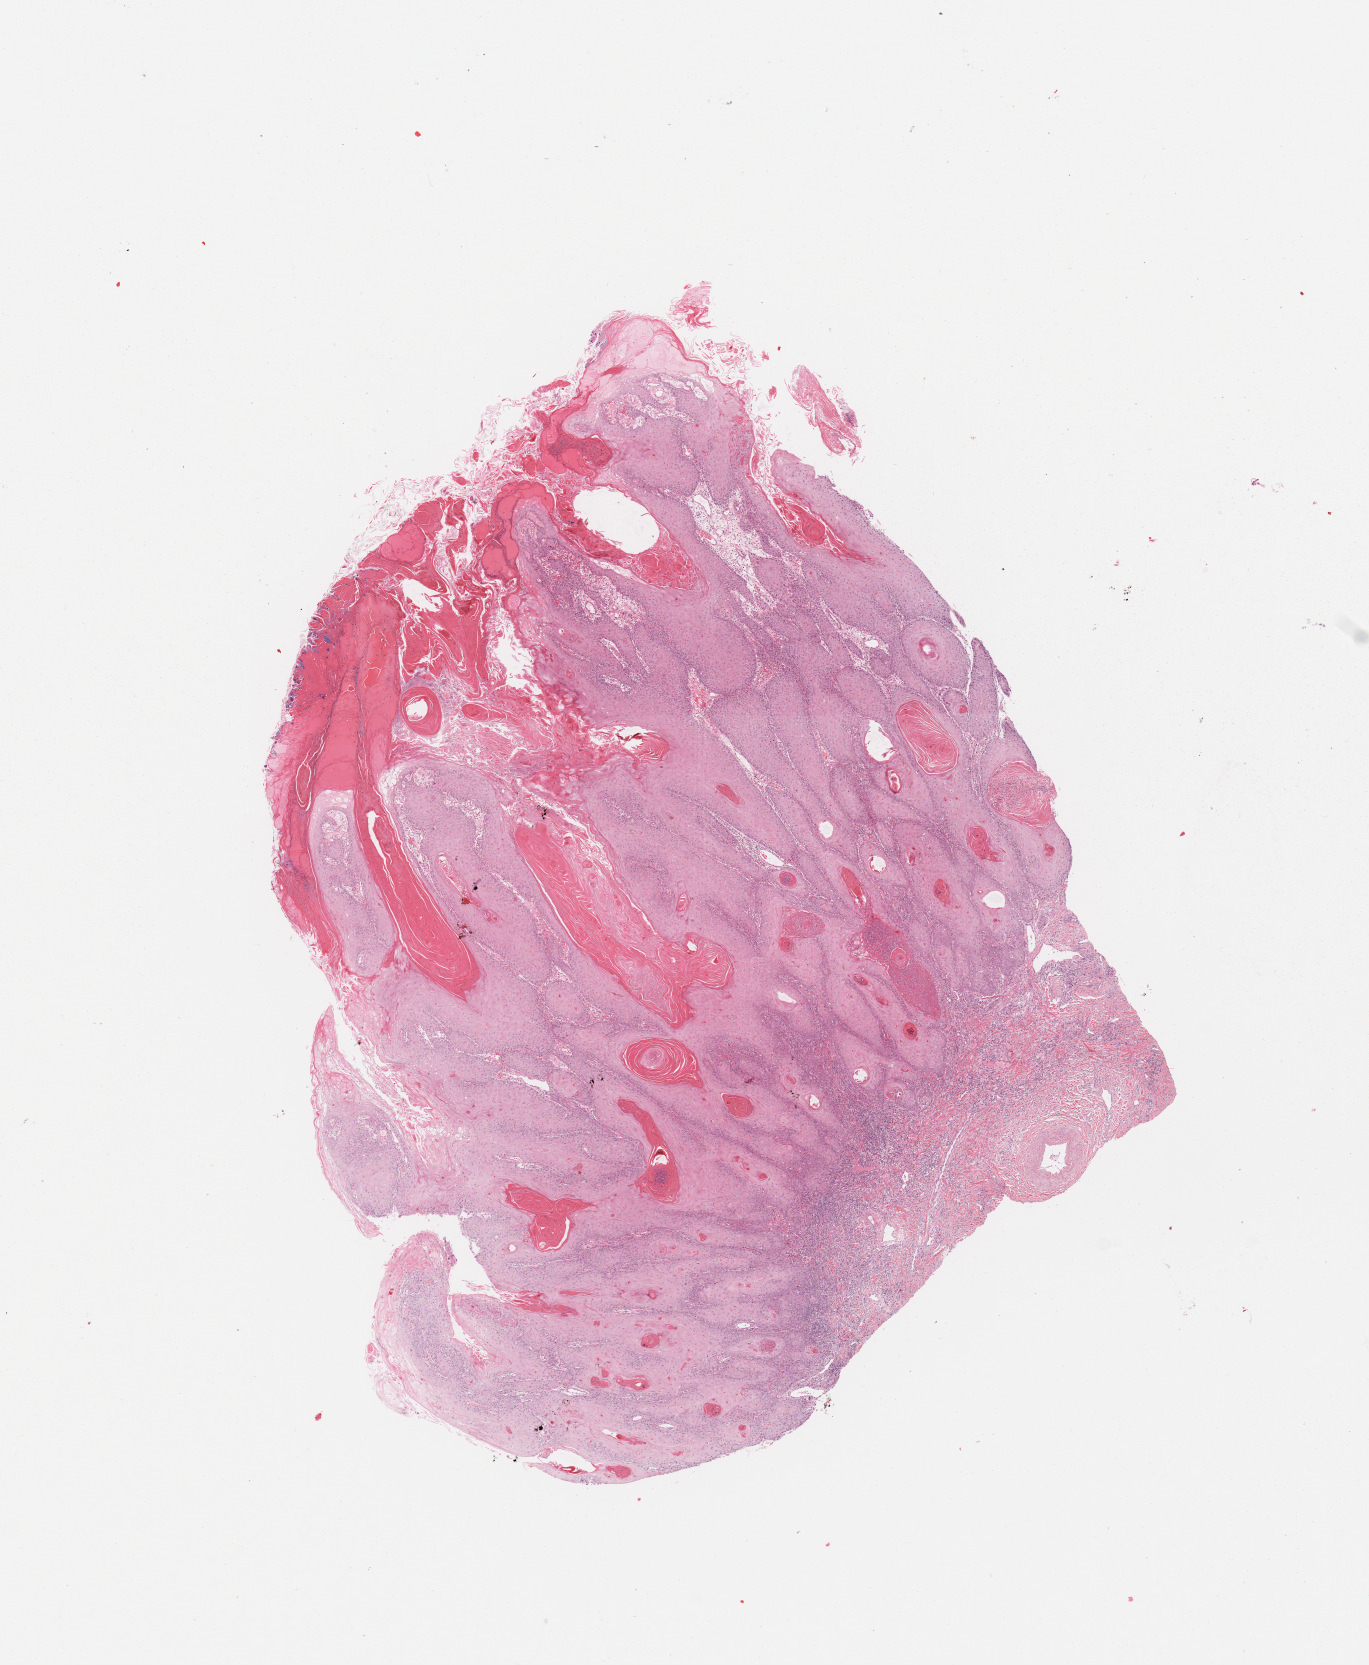
Whole-slide histology image, Hematoxylin and eosin (H&E) stained — low-resolution overview of the scanned area, about 10.8 x 13.2 mm (slide scanned at 20x); head and neck, tissue type not recorded. 54-year-old male patient.
• patient diagnosis: Squamous cell carcinoma, NOS